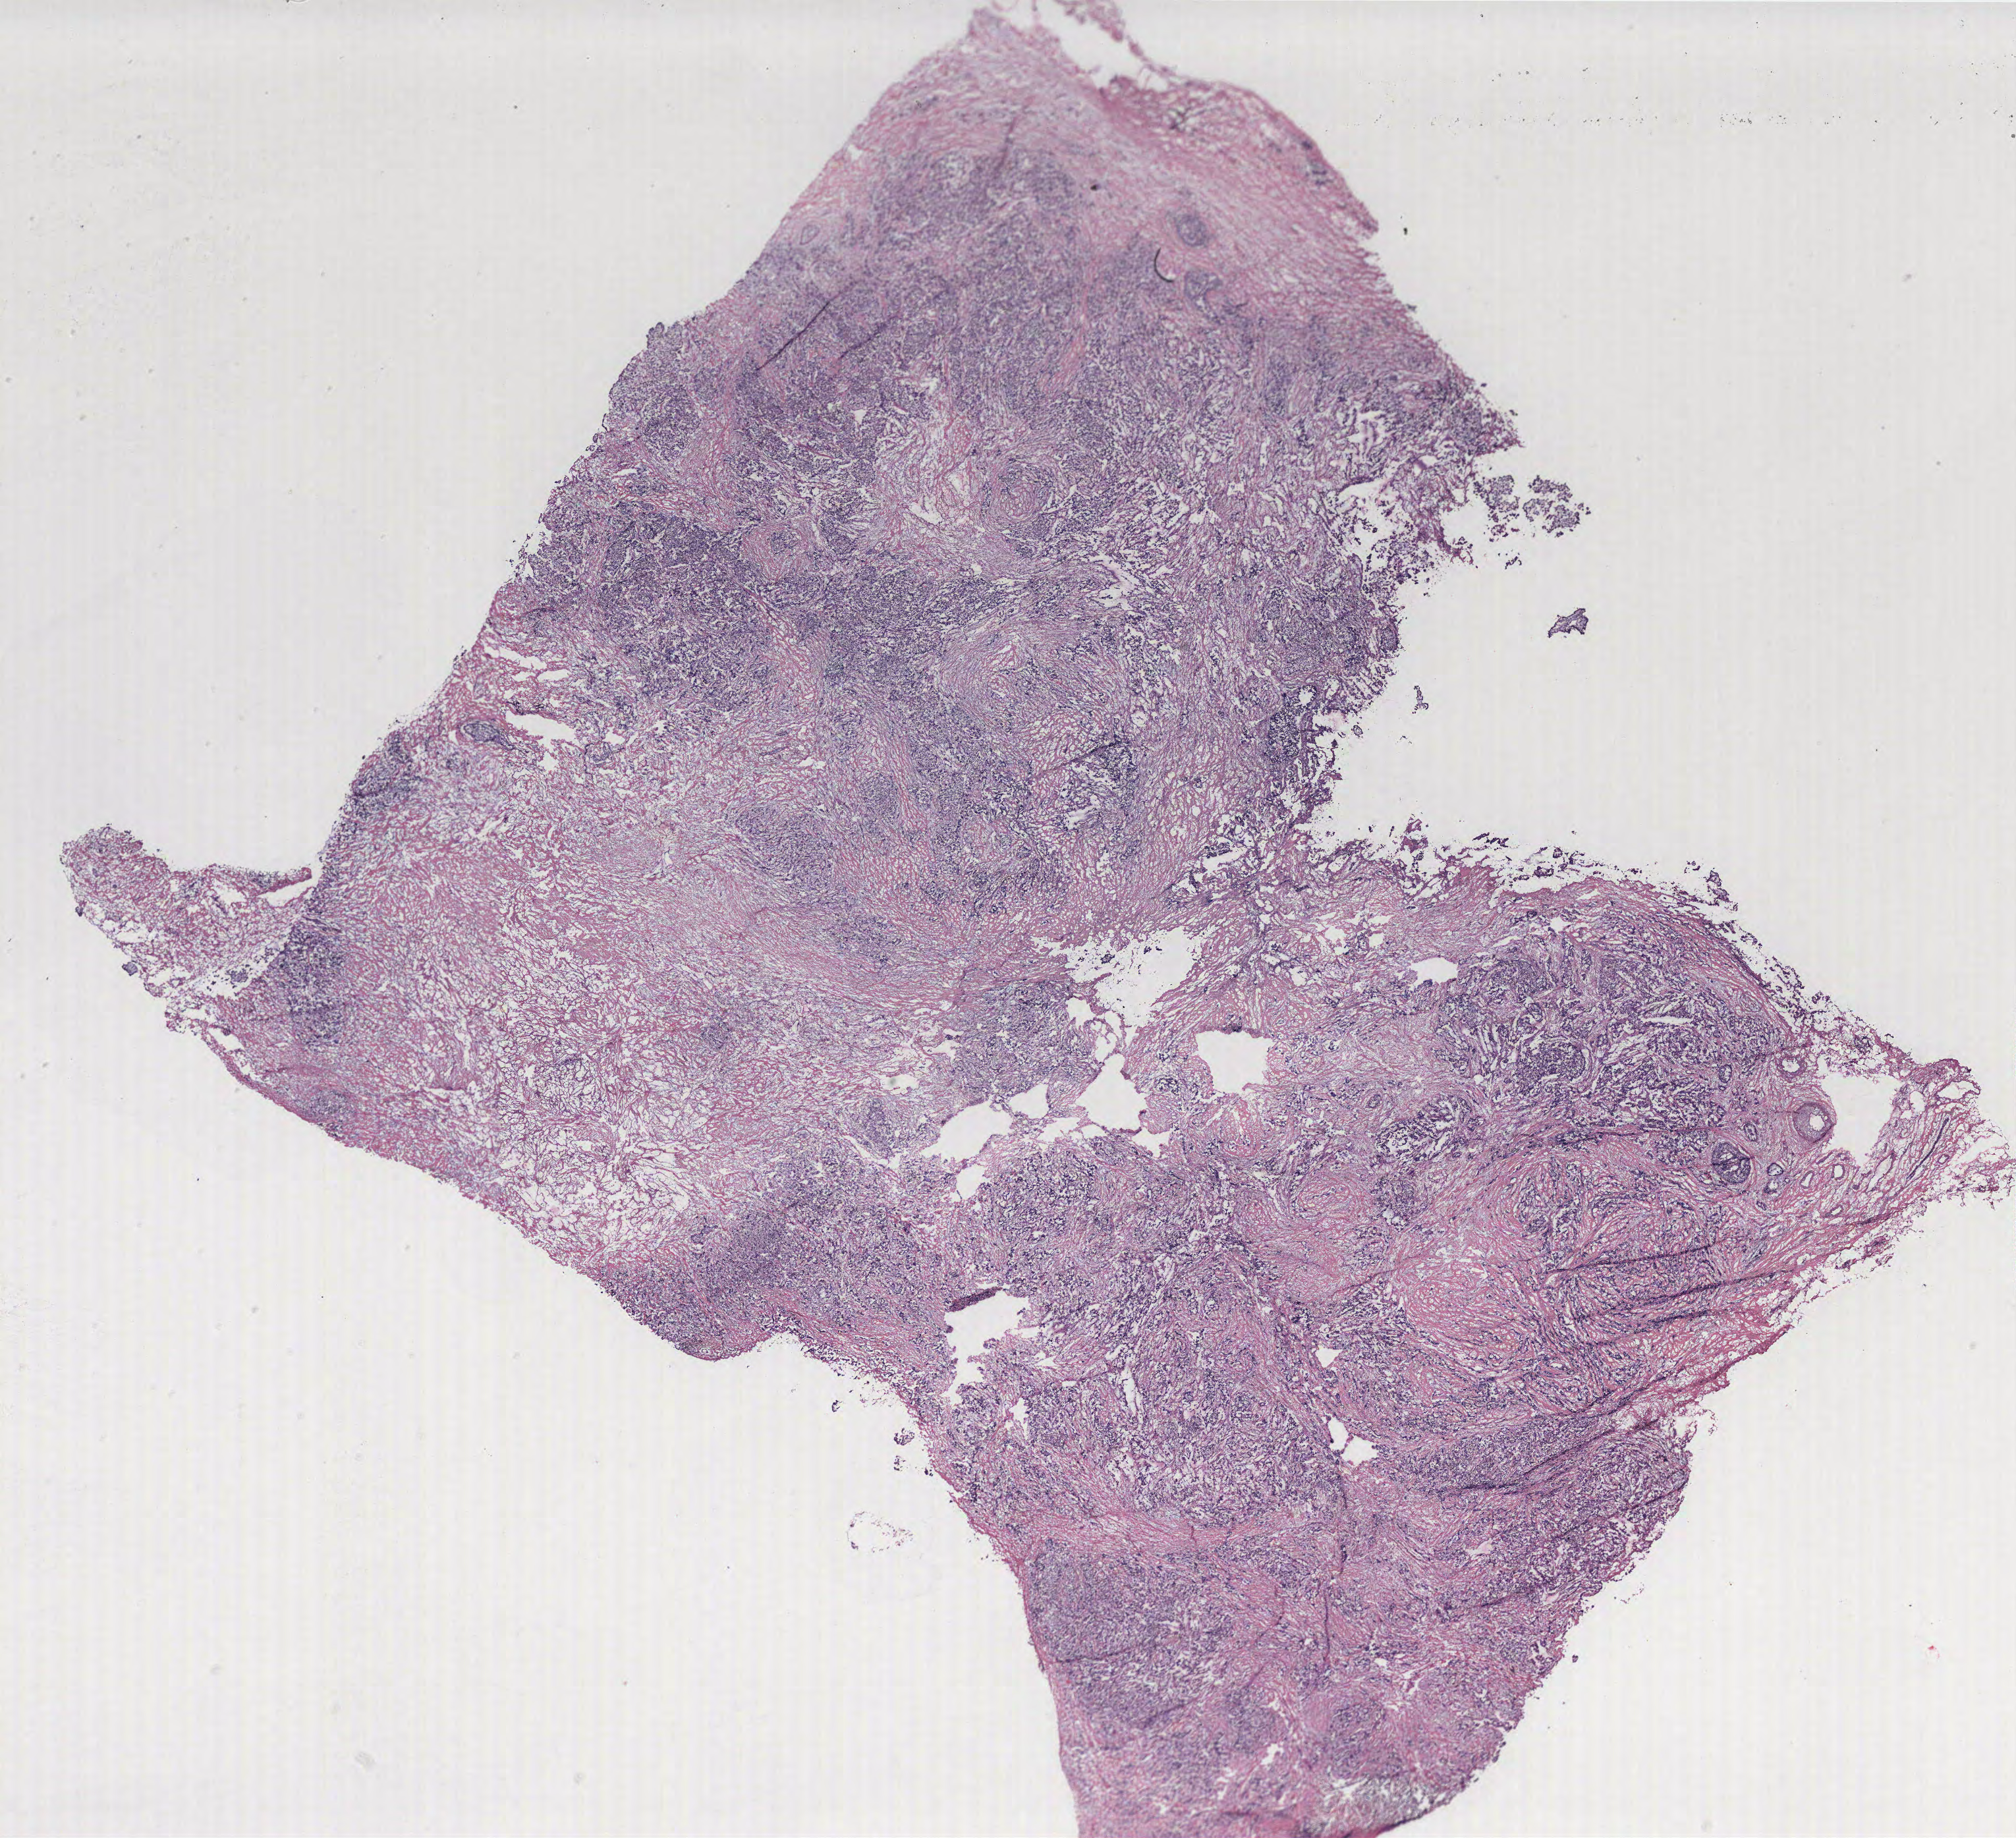
H&E-stained whole-slide image — low-resolution overview of the scanned area, about 24.5 x 22.3 mm (from a 40x scan), breast, tissue type not recorded. Patient: female, age 52 years.
Patient diagnosis: Infiltrating duct carcinoma, NOS.